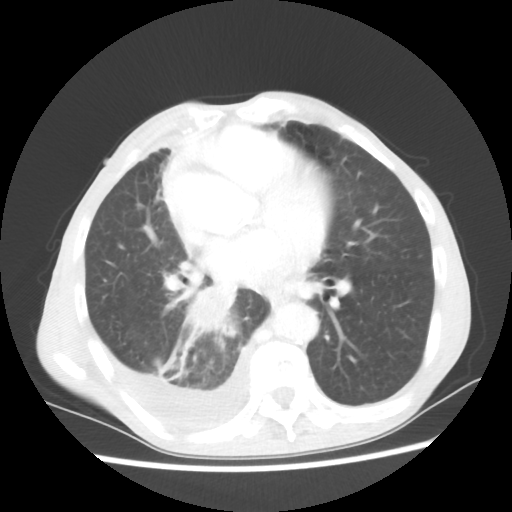
Chest CT, one axial slice. Slice 27 of 60 in the series (ordered by position). 80 kVp. Lung window (W 1500 / L -600 HU). 512 × 512 image matrix. Patient: male, 76 years. Case-level facts recorded for this patient, not image findings: clinical TNM (as recorded): T3 N3 M1a; histopathological grade: G3.
Outlined on this slice (bounding box drawn by a radiologist):
- lung tumour (recorded histology: squamous cell carcinoma): box from (x=150, y=283) to (x=248, y=389) px